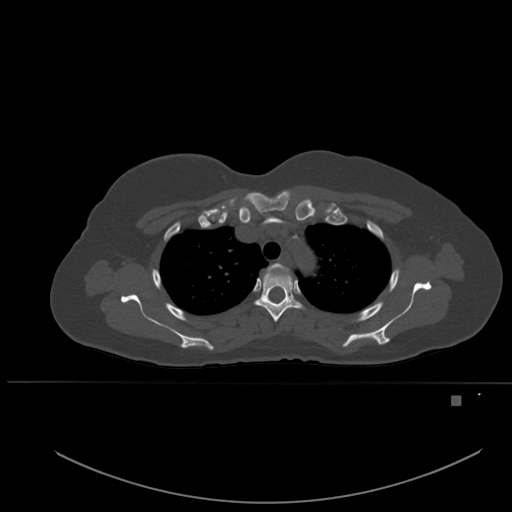
CT including the spine, one axial slice. Position 394 of 651 along the scan axis. Bone window (W 1800 / L 400 HU). 1.5 mm slice thickness. 512 × 512 image matrix, field of view 443 × 443 mm. Female patient, age 49 years. Case-level facts recorded for this patient, not image findings: primary cancer: breast; vertebrae with lytic lesions (as recorded): L3, T12, L4.
Outlined on this slice (semi-automatically segmented with operator editing):
- T2 vertebra: bounding box [x1, y1, x2, y2] px = [266, 263, 289, 273]
- T3 vertebra: [255, 270, 303, 322]